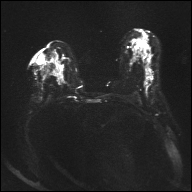
Breast MRI, one axial slice. Position 18 of 32 along the scan axis. Diffusion-weighted series; image 2 of 4 stored at this slice position (different b-values; order by instance number). 1.5 T. 4 mm slice thickness. 192 × 192 image matrix, field of view 360 × 360 mm. Female patient.
Structures marked on this image (manually delineated by an expert):
- tumour on diffusion-weighted imaging: bounding box (x1, y1, x2, y2) in pixels: (146, 80, 149, 82)